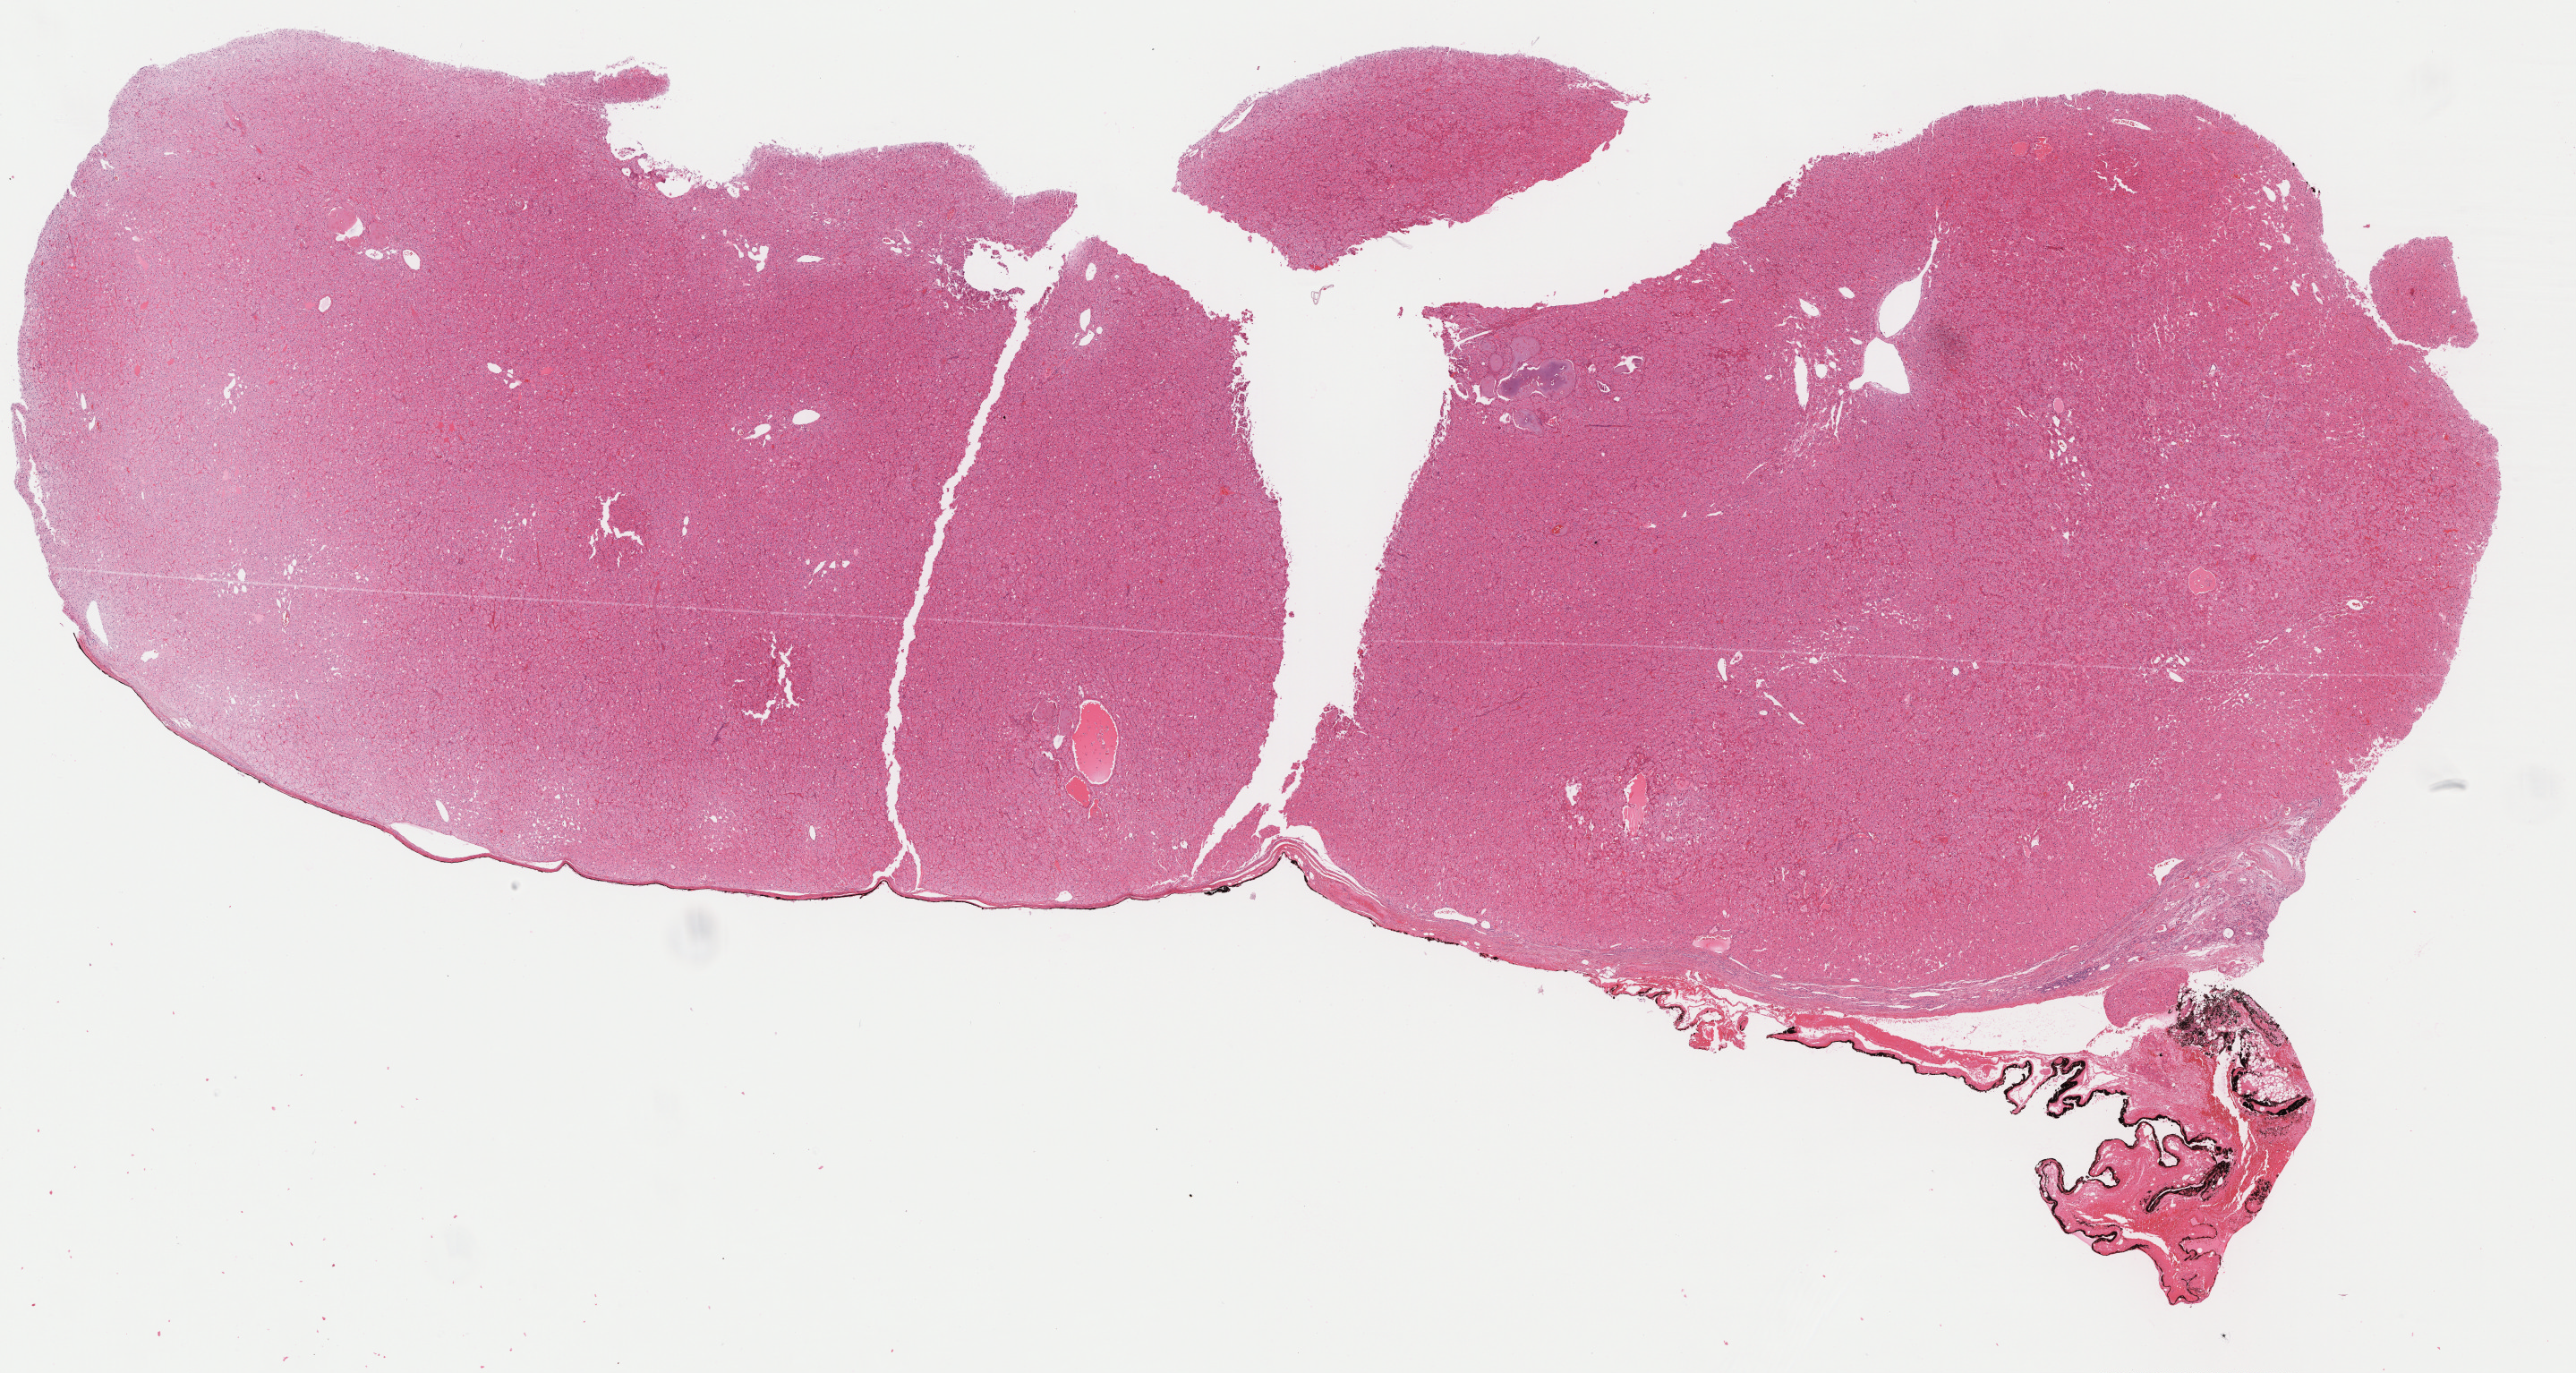
Digitized H&E tissue section (whole slide), whole scanned area (about 23.2 x 12.4 mm, acquisition: 40x scan) shown as a low-resolution overview, formalin-fixed paraffin-embedded (FFPE) diagnostic section, kidney, primary tumour sample. Patient: female, age at initial diagnosis 42 years.
* histologic diagnosis: Renal cell carcinoma, chromophobe type
* AJCC pathologic stage: I (6th edition)
* laterality: right